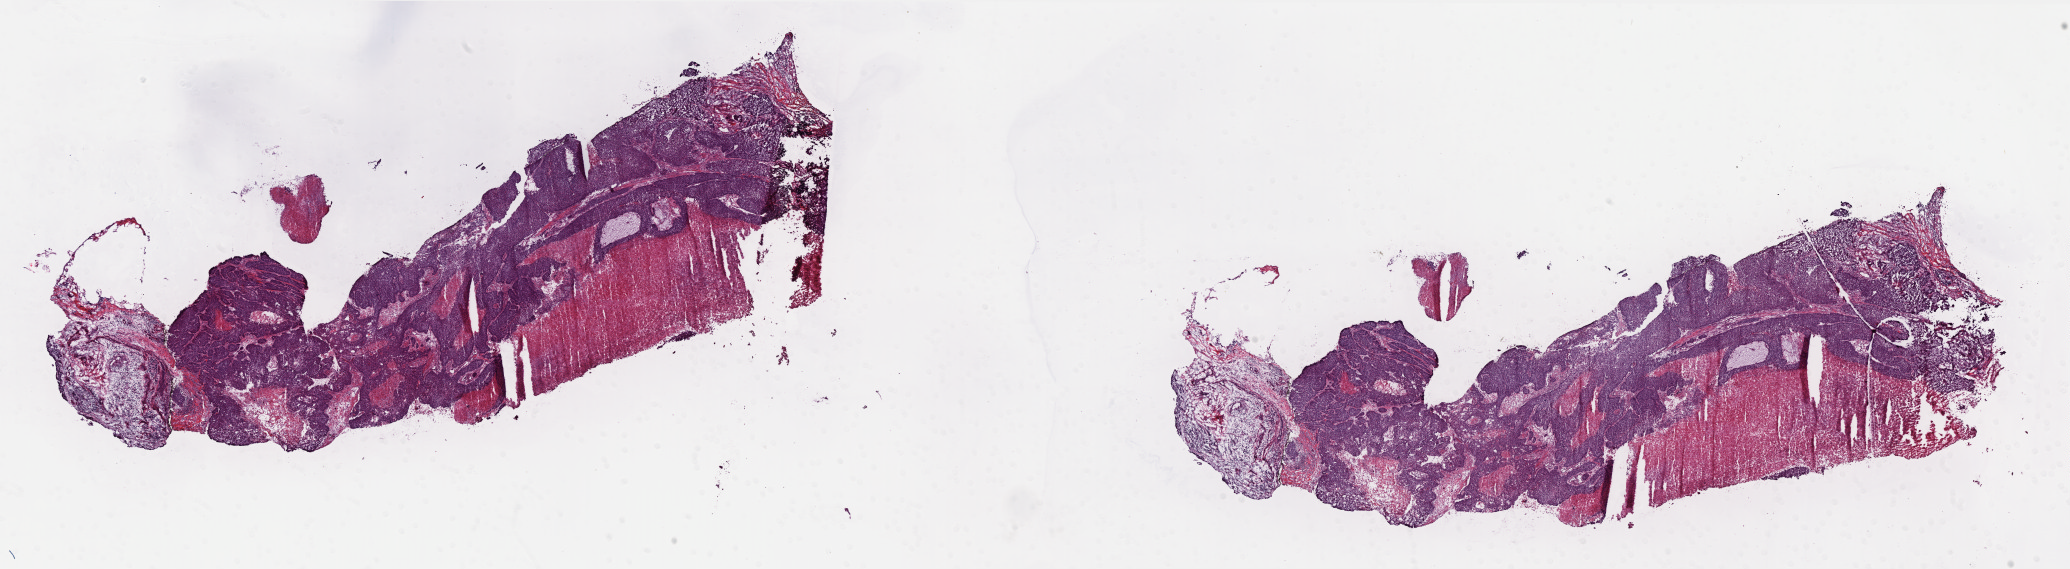
Digitized Hematoxylin and eosin (H&E) stained tissue section (whole slide), low-resolution overview of the scanned area, about 33.2 x 9.1 mm (from a 40x scan); frozen section; primary tumour sample from the breast. Patient: female, age at initial diagnosis 57 years. Pathologist review of this section (percent, as recorded): tumour cells 65%, tumour nuclei 80%, normal cells 0%, stromal cells 15%, necrosis 20%. Infiltration values recorded for this section: lymphocyte infiltration 12%, monocyte infiltration 1%, neutrophil infiltration 1%.
Laterality: left. Lymph nodes positive (case pathology): 0 of 1 examined. Pathologic diagnosis: Infiltrating duct carcinoma, NOS. AJCC pathologic stage: IIA.